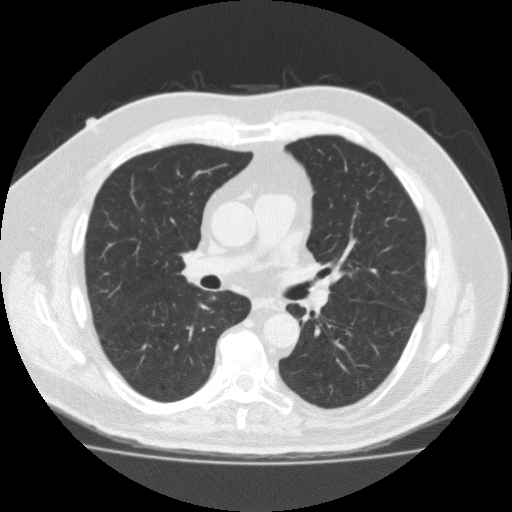
Axial slice from a low-dose chest CT screening exam. Third annual screen. Lung window (W 1500 / L -600 HU). 2 mm slice thickness. Male participant, aged 56 years at enrolment.
Expert-annotated lung lesion, bounding box <188,281,228,316> (left, top, right, bottom; pixels). Screening reader's record for this exam (one nodule recorded; not confirmed to be the boxed lesion): non-calcified nodule or mass ≥4 mm, right lower lobe, 12 × 8 mm, spiculated (stellate) margins, soft tissue attenuation, pre-existing on the prior screen: yes; interval growth: yes. Participant outcome: lung cancer diagnosed 49 days after this screen — adenocarcinoma, NOS, right lower lobe, moderately differentiated (G2), stage IA (AJCC 6th edition), 12 mm at pathology.